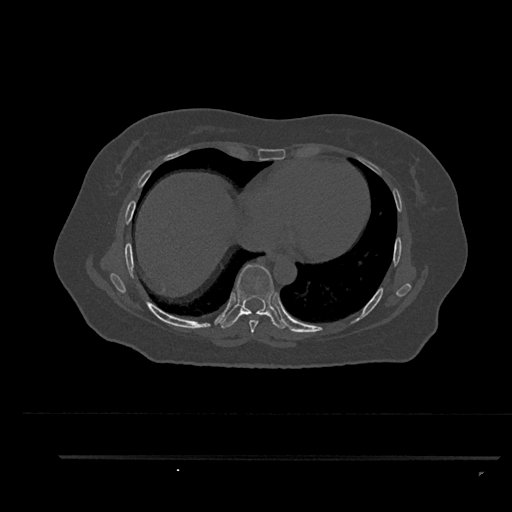
CT including the spine, one axial slice; position 476 of 797 along the scan axis; reconstruction kernel Br40s/3; bone window (W 1800 / L 400 HU); 0.5 mm slice thickness; 512 × 512 image matrix, field of view 408 × 408 mm. Patient: female, 44 years. From the clinical record (not read from this slice): primary cancer: renal.
Outlined on this slice (semi-automatically segmented with operator editing):
- T7 vertebra: bounding box <249,320,259,333> (left, top, right, bottom; pixels)
- T8 vertebra: <220,264,287,329>